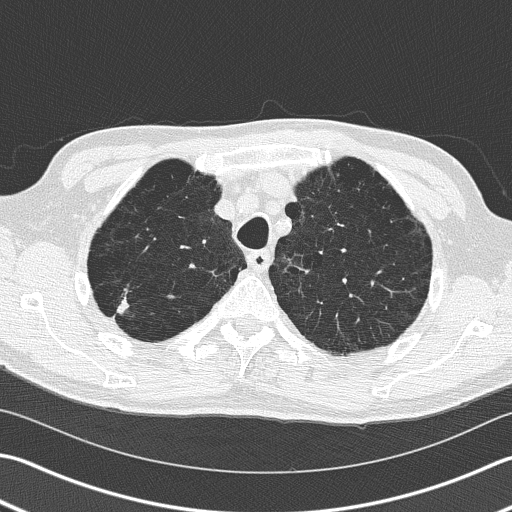
Chest CT (low-dose screening protocol), one axial image. Baseline annual screen. Lung window (W 1500 / L -600 HU). 512 × 512 image matrix. Male participant, aged 66 years at enrolment. Current smoker at enrolment.
Lesion marked by an expert reader, bounding box [x1, y1, x2, y2] px = [95, 279, 149, 339]. Reader record for this screening exam (exam-level; its link to the box is not recorded): non-calcified nodule or mass ≥4 mm, right upper lobe, 39 × 23 mm, spiculated (stellate) margins, soft tissue attenuation. Later outcome: lung cancer diagnosed 36 days after this screen — squamous cell carcinoma, NOS, right upper lobe, poorly differentiated (G3), stage IB (AJCC 6th edition), 23 mm at pathology.